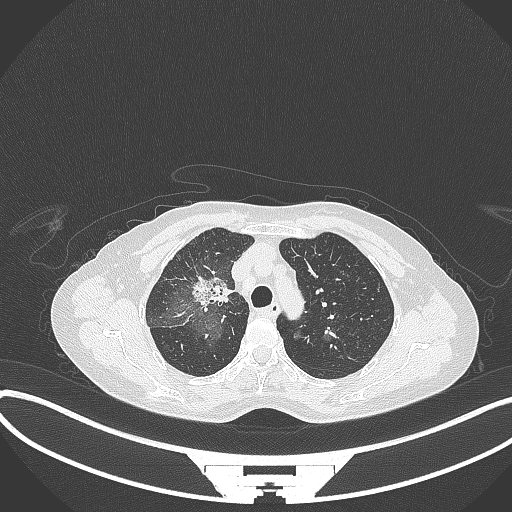
Chest CT, one axial slice; slice 240 of 284 in the series (ordered by position); 120 kVp; lung window (W 1500 / L -600 HU); 1 mm slice thickness; 512 × 512 image matrix, field of view 400 × 400 mm. Female patient, age 59 years. Case-level facts recorded for this patient, not image findings: clinical TNM (as recorded): T3 N0 M0; histopathological grade: G1.
Structures marked on this image (bounding box drawn by a radiologist):
- lung tumour (recorded histology: adenocarcinoma): box from (x=191, y=273) to (x=232, y=311) px